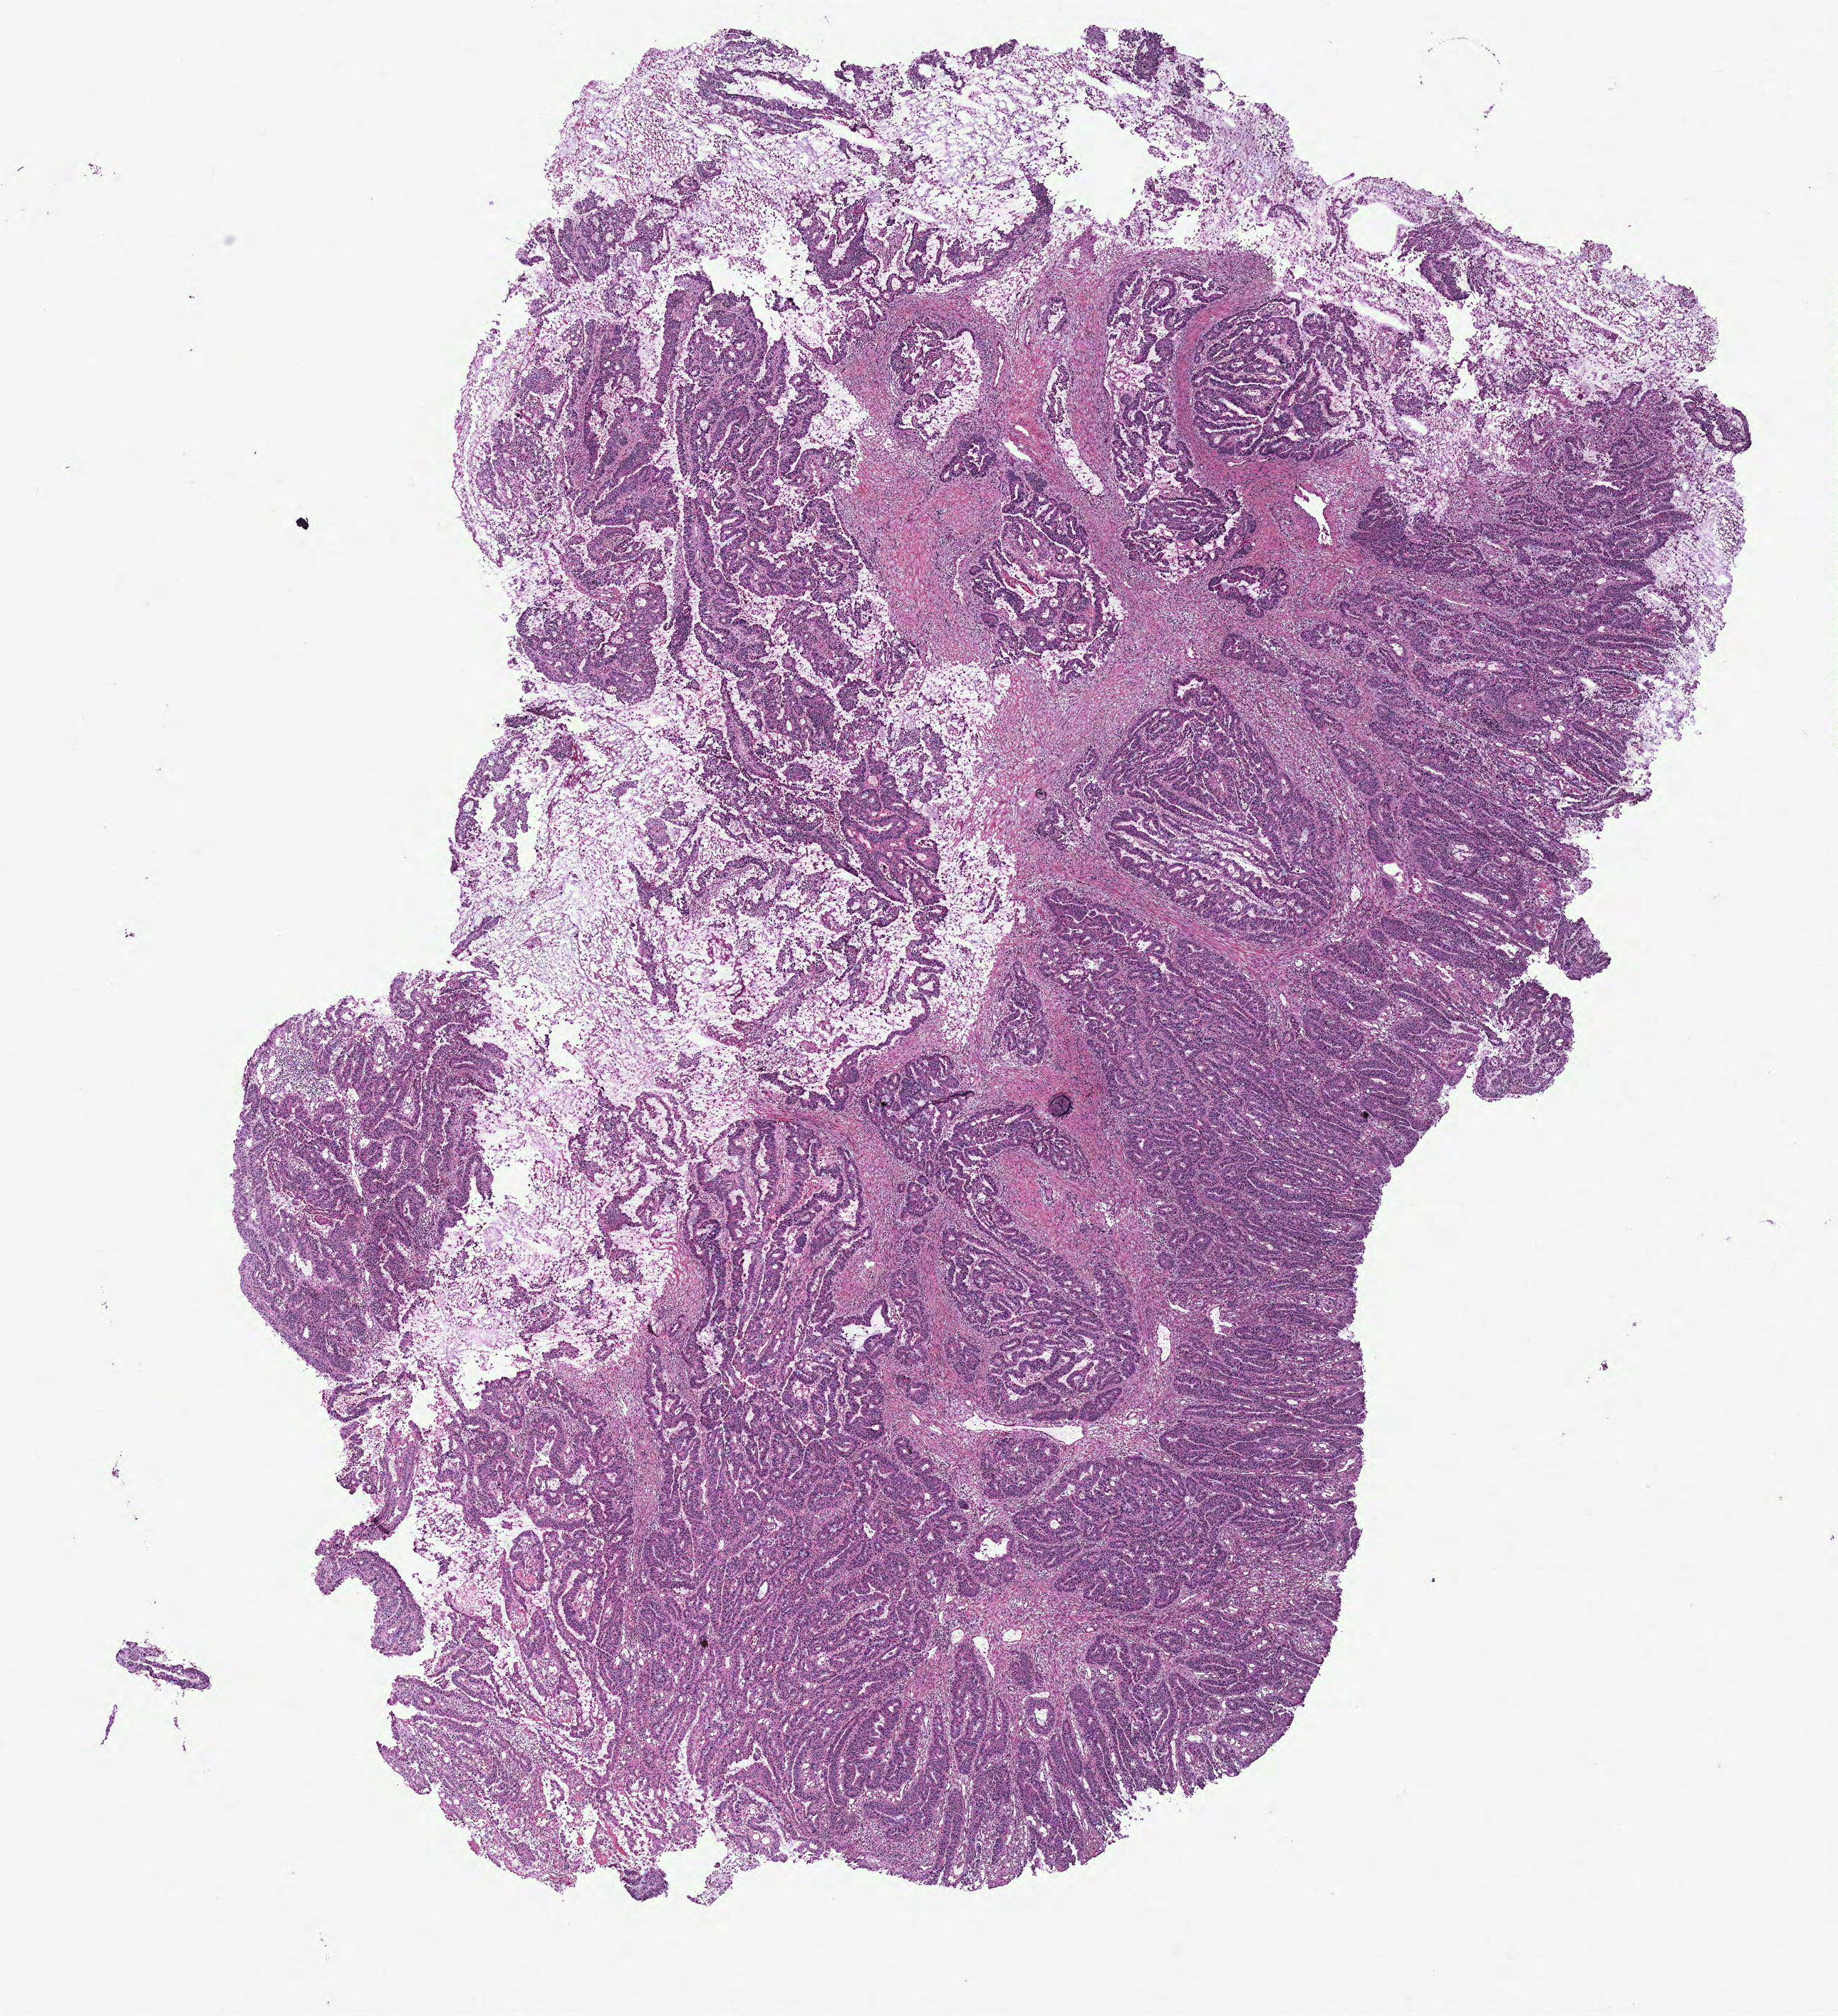
Whole-slide histology image, H&E-stained, low-resolution overview of the scanned area, about 10.3 x 11.3 mm (slide scanned at 40x). Tumour tissue sample, colon. 71-year-old female patient.
Histologic diagnosis: Adenocarcinoma, NOS. AJCC pathologic stage: IIB. Primary tumour site (as recorded): colon.